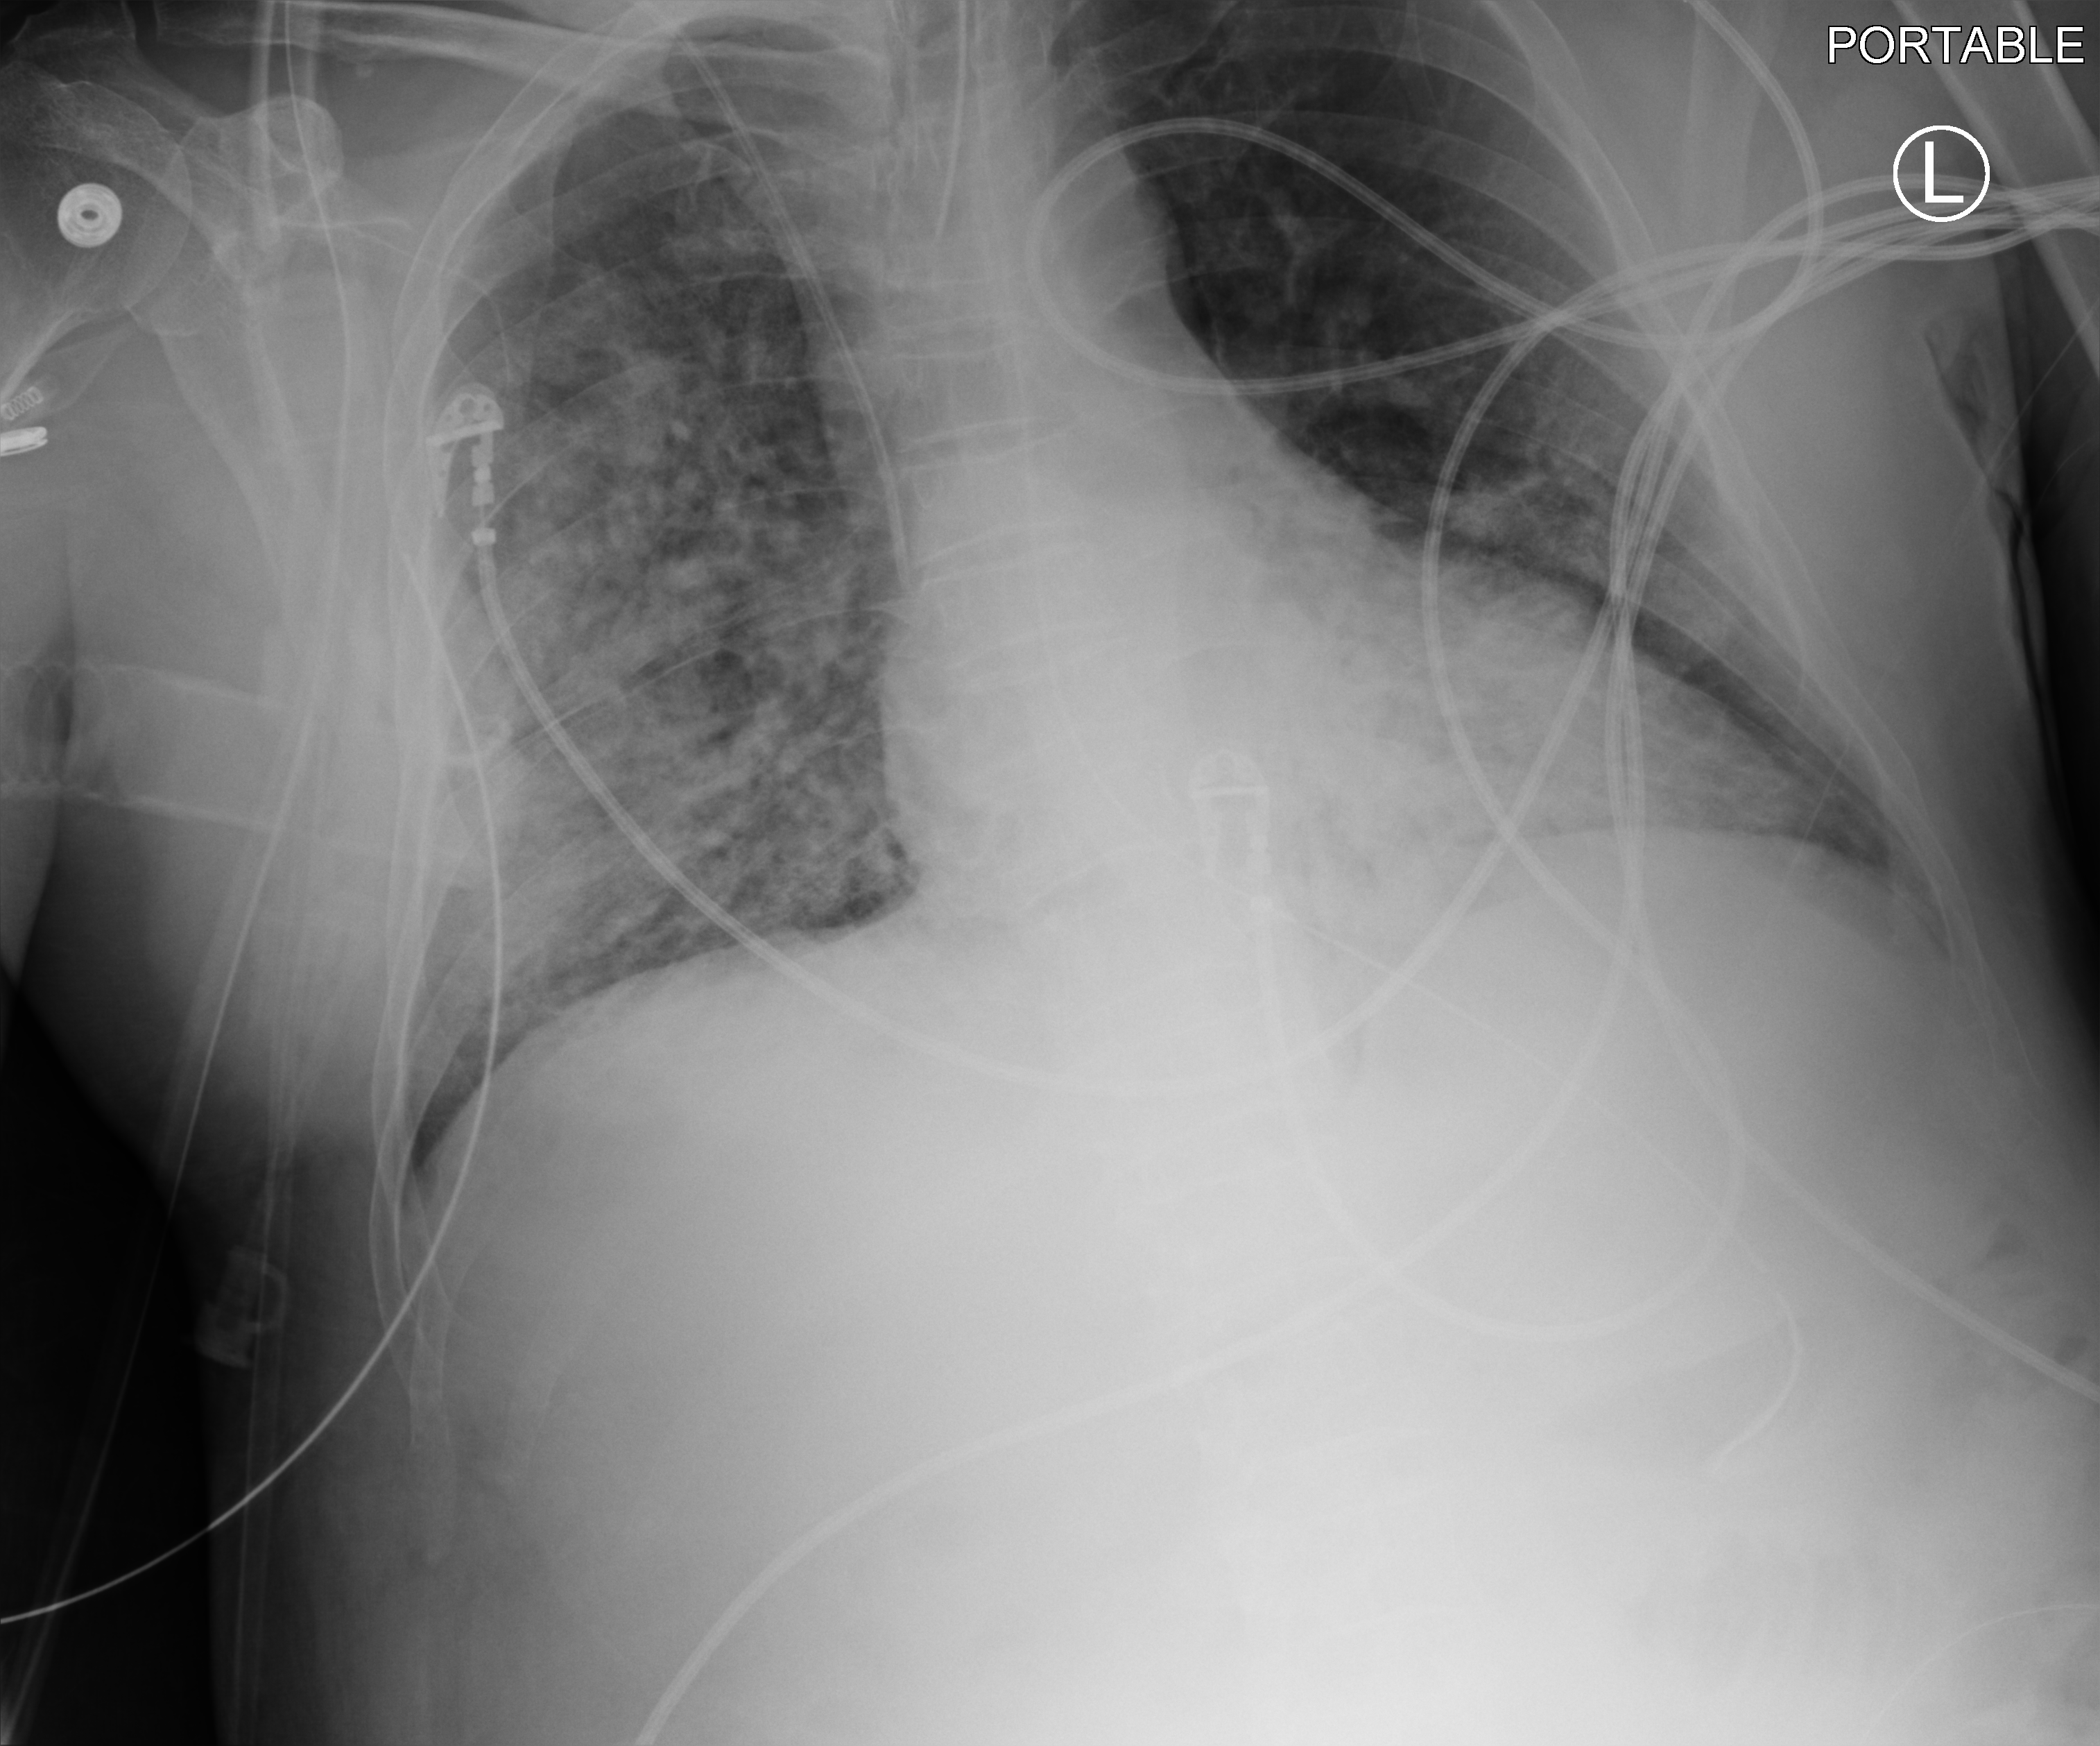
Chest X-ray (portable), anteroposterior (AP) projection. Male patient hospitalised with COVID-19, age 60–74 years.
From the hospital-stay record, not from the radiograph (when in the stay this image was taken is not recorded): length of hospital stay: 19 days.